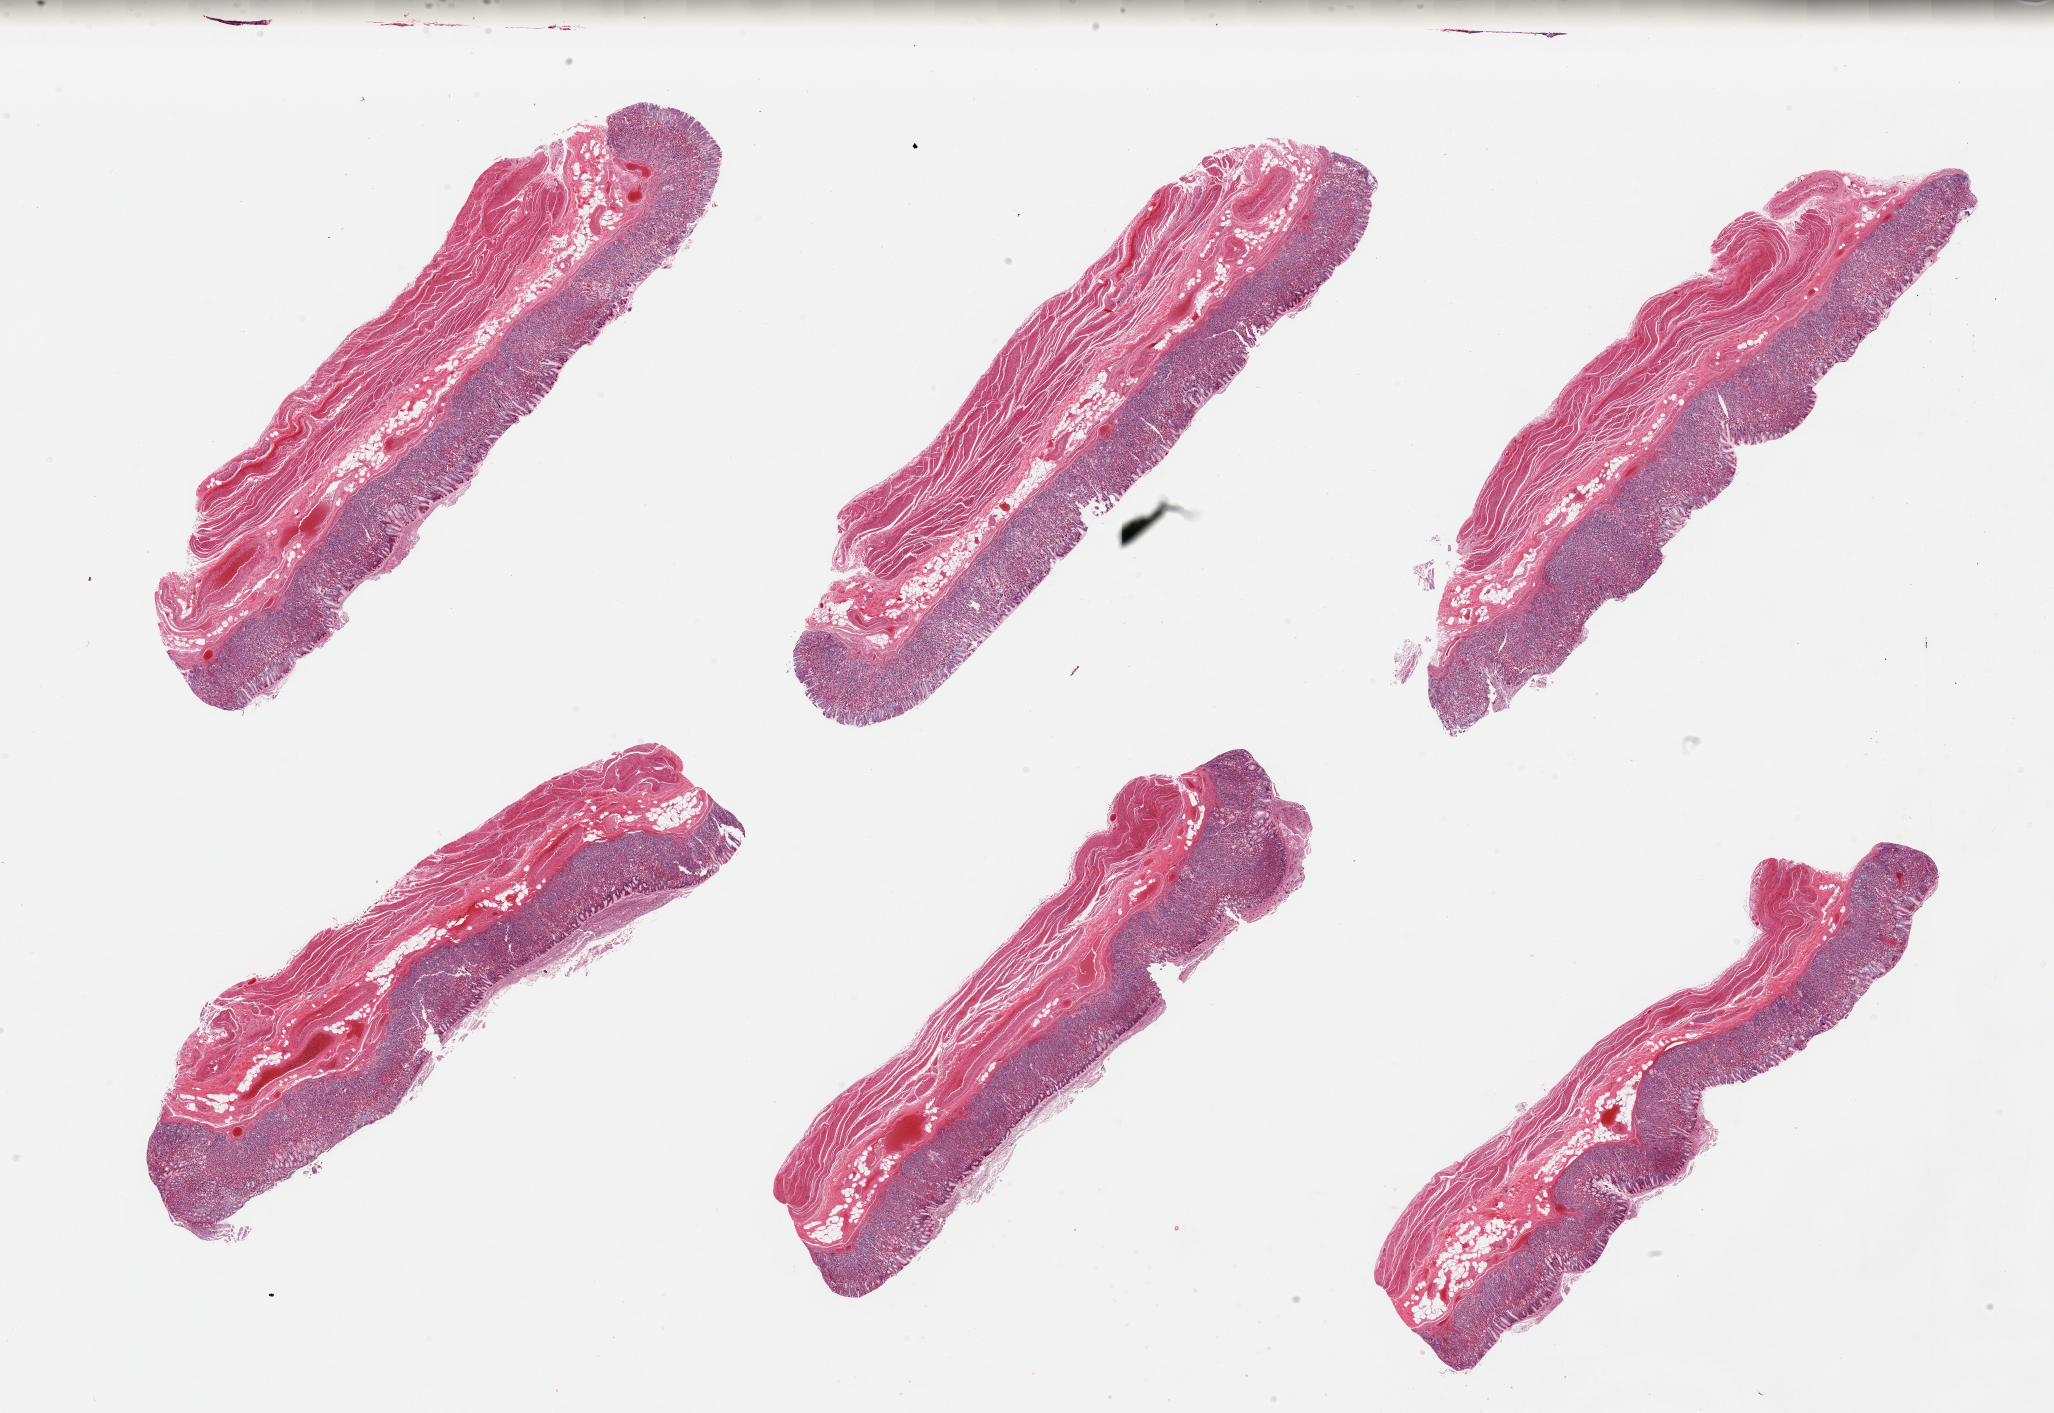
Digitized H&E-stained section, whole scanned area (about 32.5 x 22.3 mm, slide scanned at 20x) shown as a low-resolution overview; PAXgene-fixed paraffin-embedded (PFPE) section; section of stomach (target tissue); donor tissue sample. Donor sex: male.
Pathologist's review note for this sample: 6 pieces; full thickness sections.